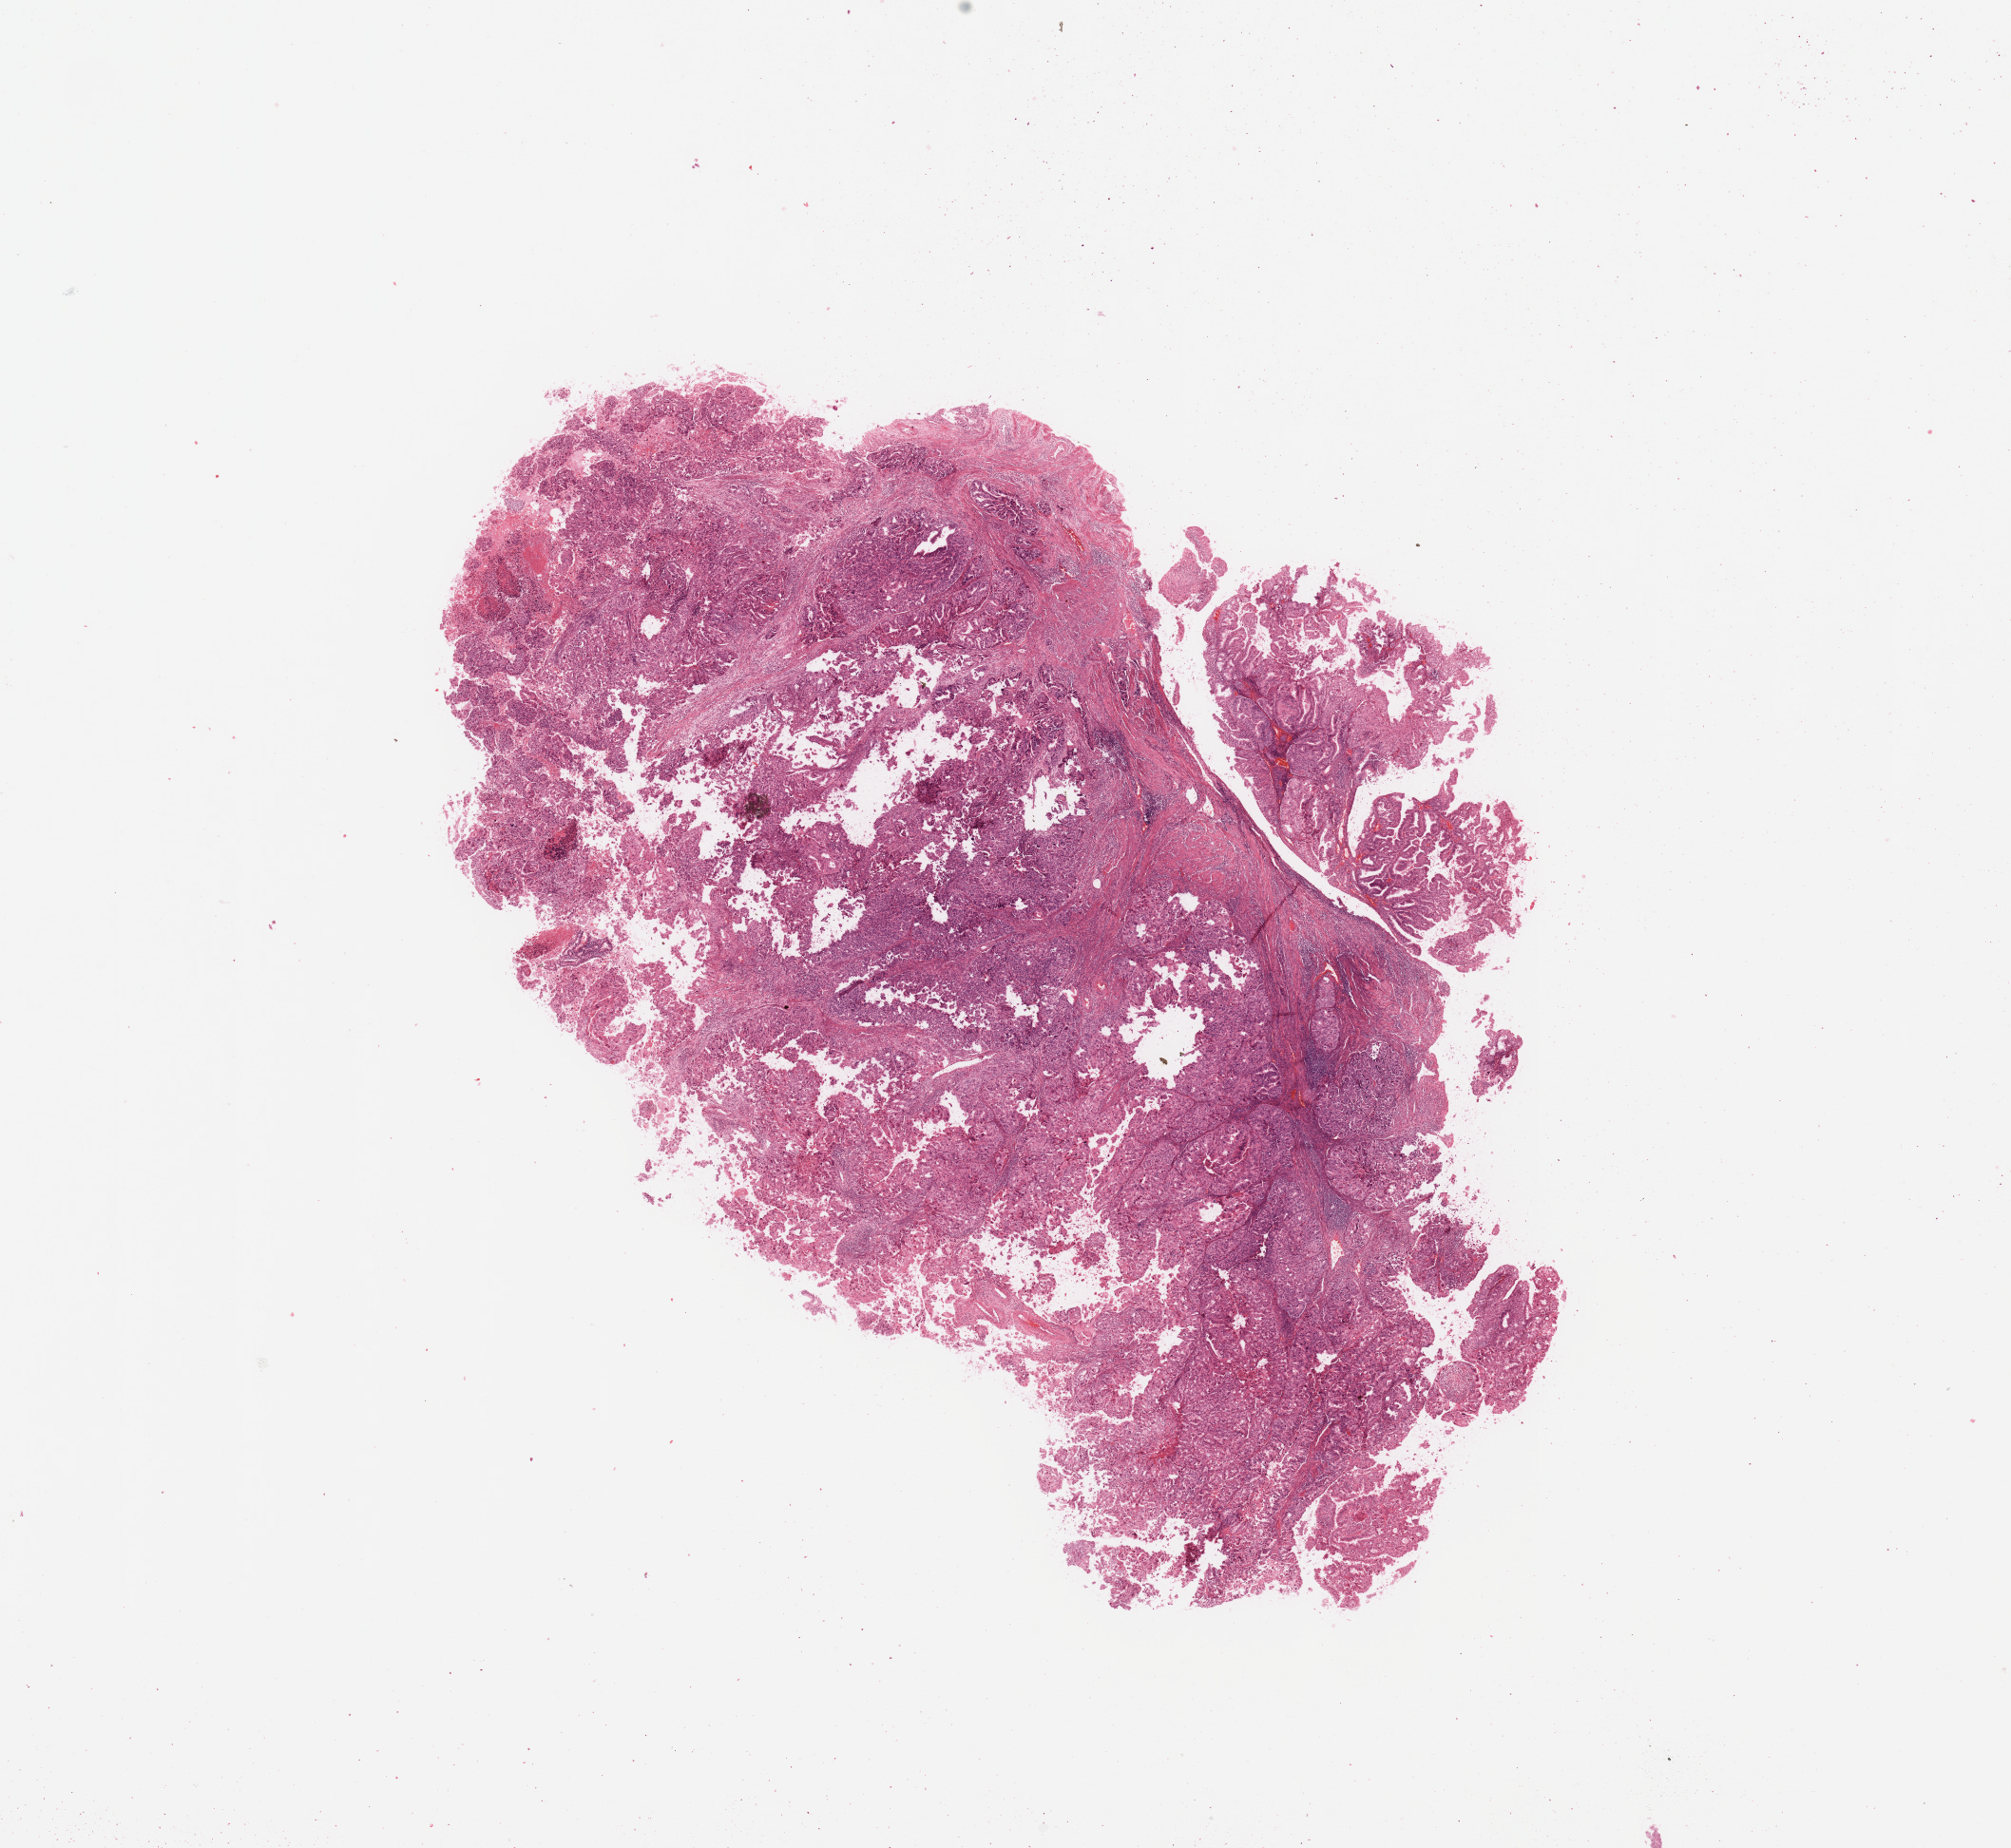
Hematoxylin and eosin (H&E) stained whole-slide image — a low-resolution overview of the entire scanned area, about 16.7 x 15.4 mm (from a 20x scan); tumour tissue sample, sampled site: uterus. Patient: female, age 60 years. Histologic grade: G3 (poorly differentiated). Composition of this section per pathologist review: tumour nuclei 80%, necrosis 10%.
- diagnosis: Endometrioid adenocarcinoma, NOS
- AJCC pathologic stage: I